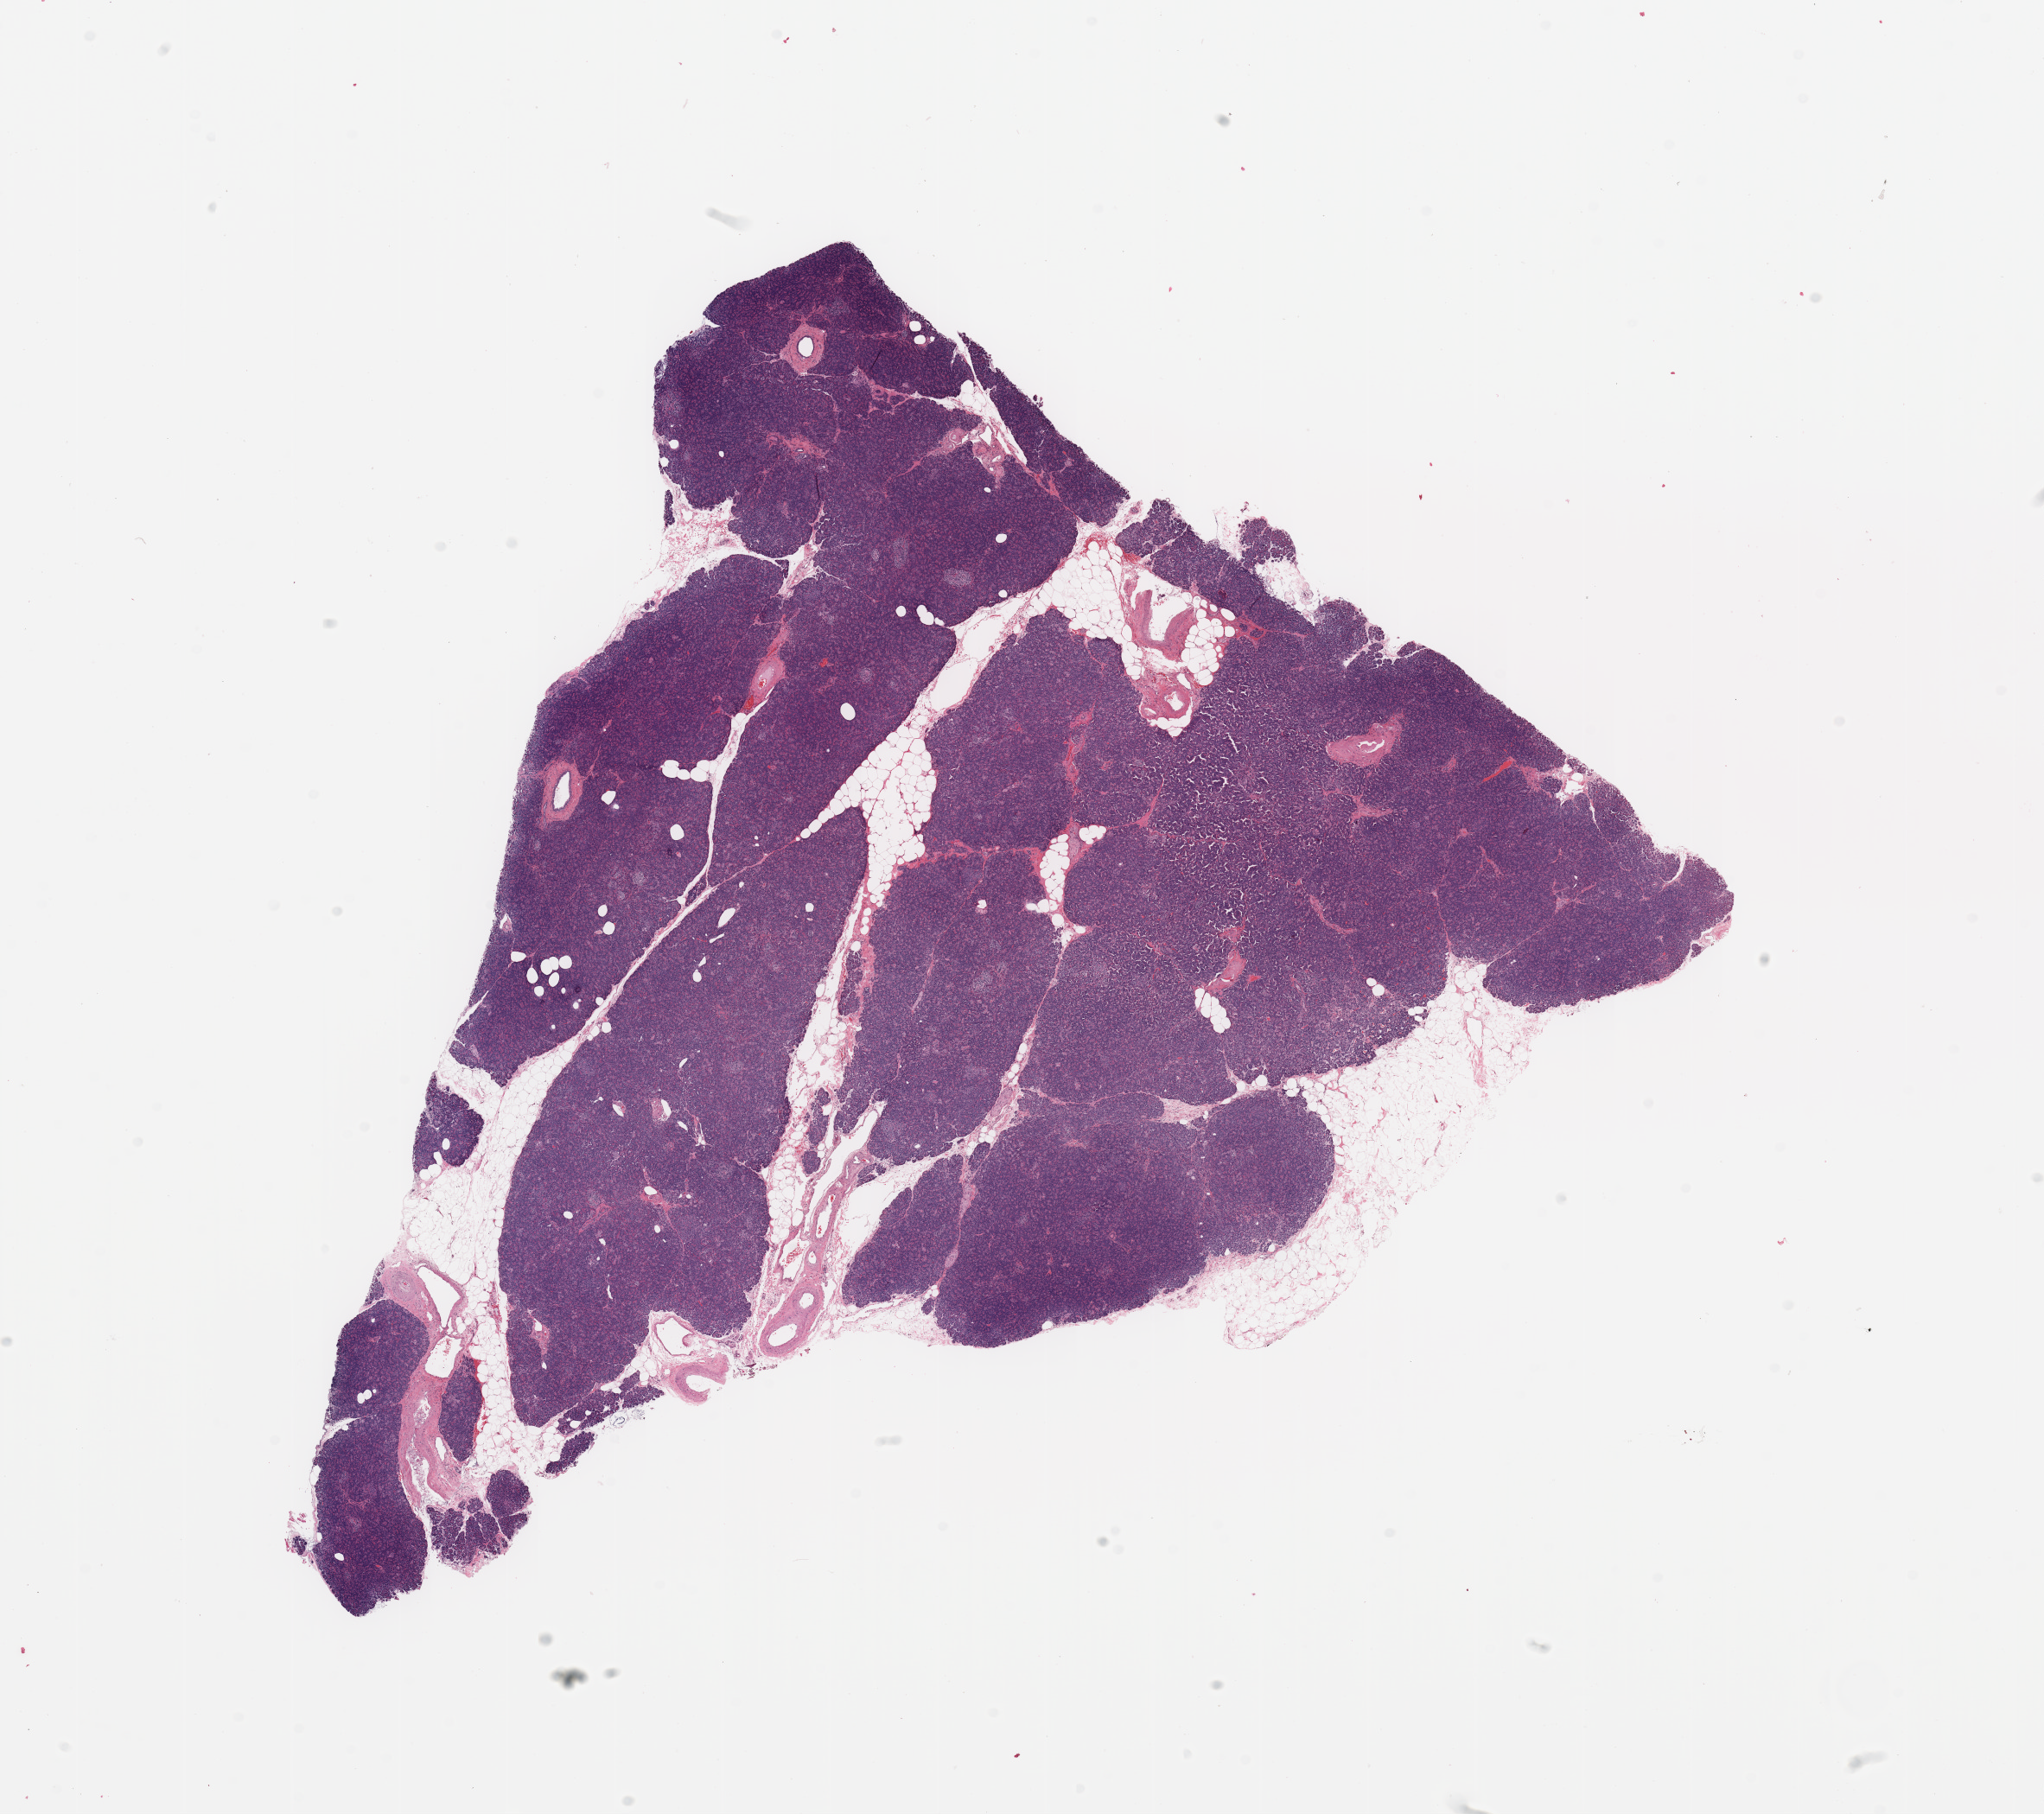
H&E whole-slide image, whole scanned area (about 18.7 x 16.6 mm) shown as a low-resolution overview. Normal (non-tumour) tissue sample, sampled site: pancreas. 68-year-old male patient.
This section: normal (non-tumour) tissue from the same patient. Patient diagnosis: Infiltrating duct carcinoma, NOS.